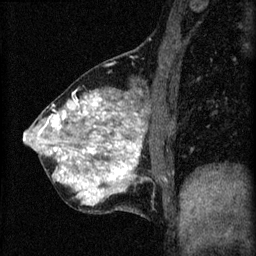
Breast MRI (dynamic contrast-enhanced), one sagittal slice. Position 21 of 60 along the scan axis. 3 images stored at this slice position (order not interpretable as contrast timing). 1.5 T. TE 4.2 ms, TR 8.2 ms. 2 mm slice thickness. 256 × 256 image matrix, field of view 180 × 180 mm. Patient: female, 40 years.
Structures marked on this image (semi-automatically segmented with operator editing):
- analysis volume of interest (the breast-tissue region the enhancement analysis was run in; not a lesion): box from (x=24, y=80) to (x=173, y=217) px
- tumour enhancement mask (voxels above the 70 % enhancement threshold inside the analysis volume of interest): (x=26, y=94)–(x=141, y=207)